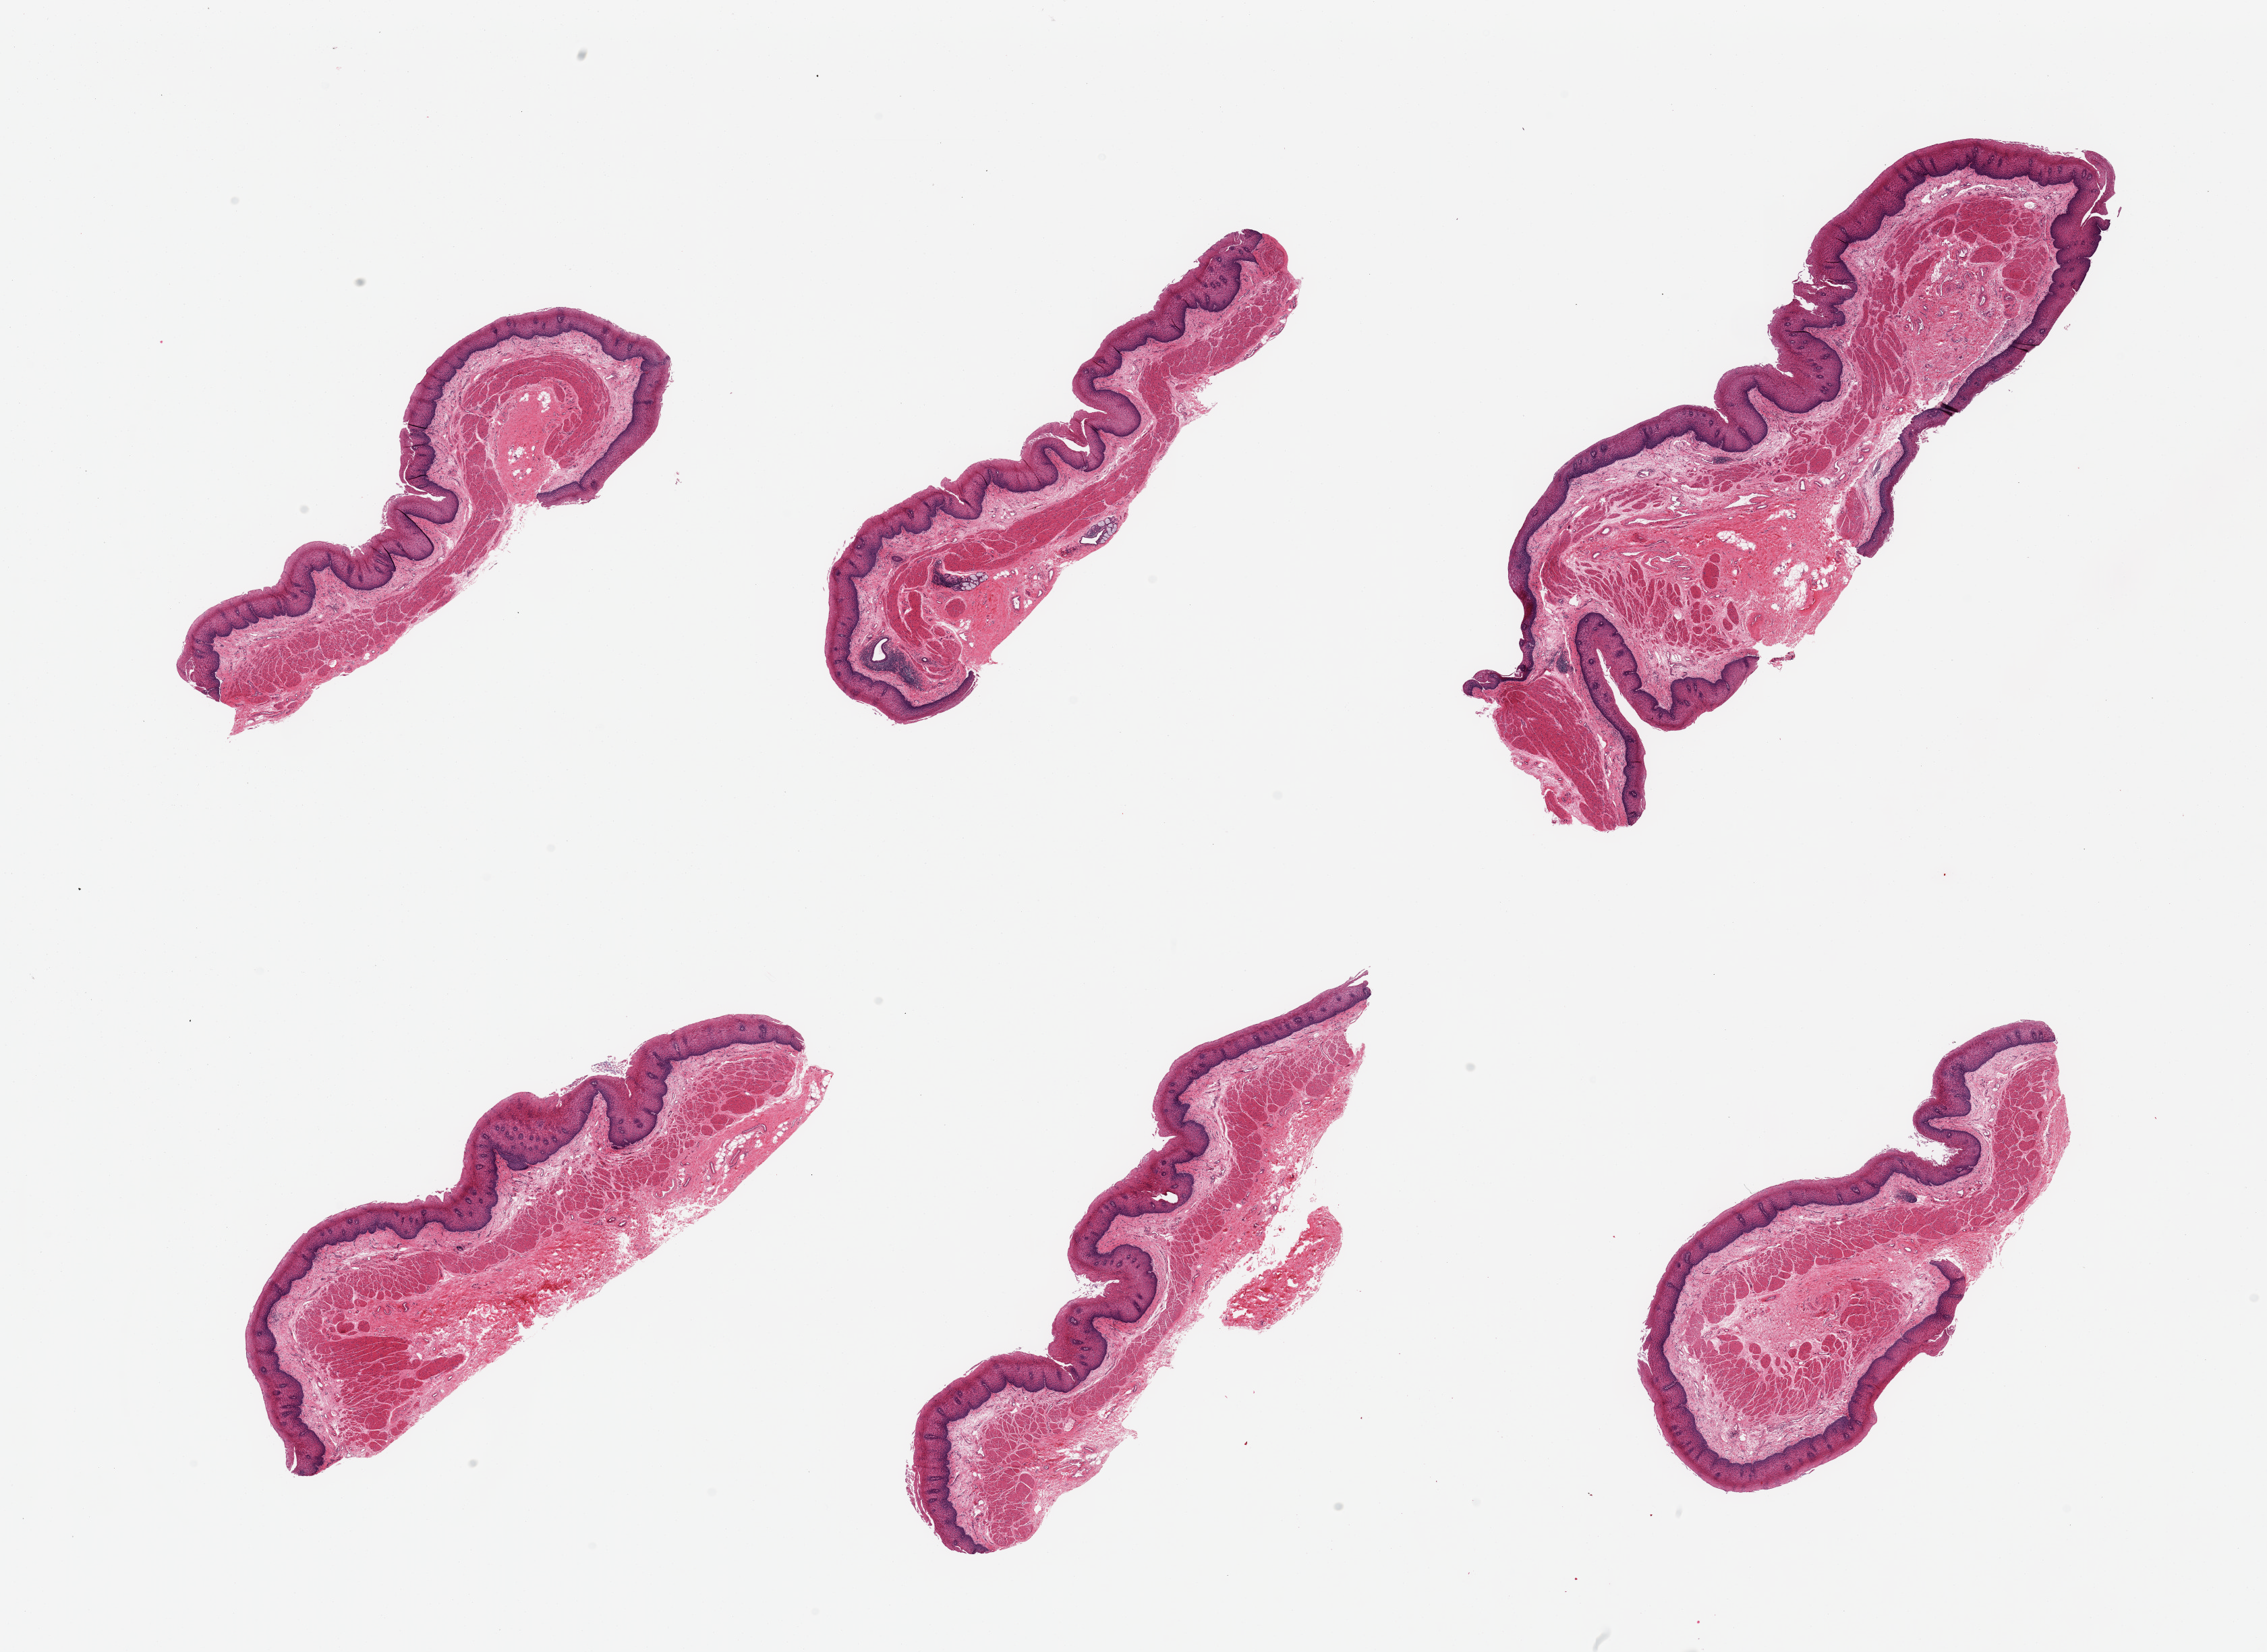
Whole-slide image, hematoxylin and eosin (H&E) stain — whole scanned area (about 26.6 x 19.4 mm, slide scanned at 20x) shown as a low-resolution overview, PAXgene-fixed, paraffin-embedded tissue, section of esophageal mucous membrane (target tissue), donor tissue sample. Donor sex: male.
Review note (as recorded): 6 pieces, squamous mucosa up to ~0.8mm, 20-30% thickness; Few submucosal mucus glands.